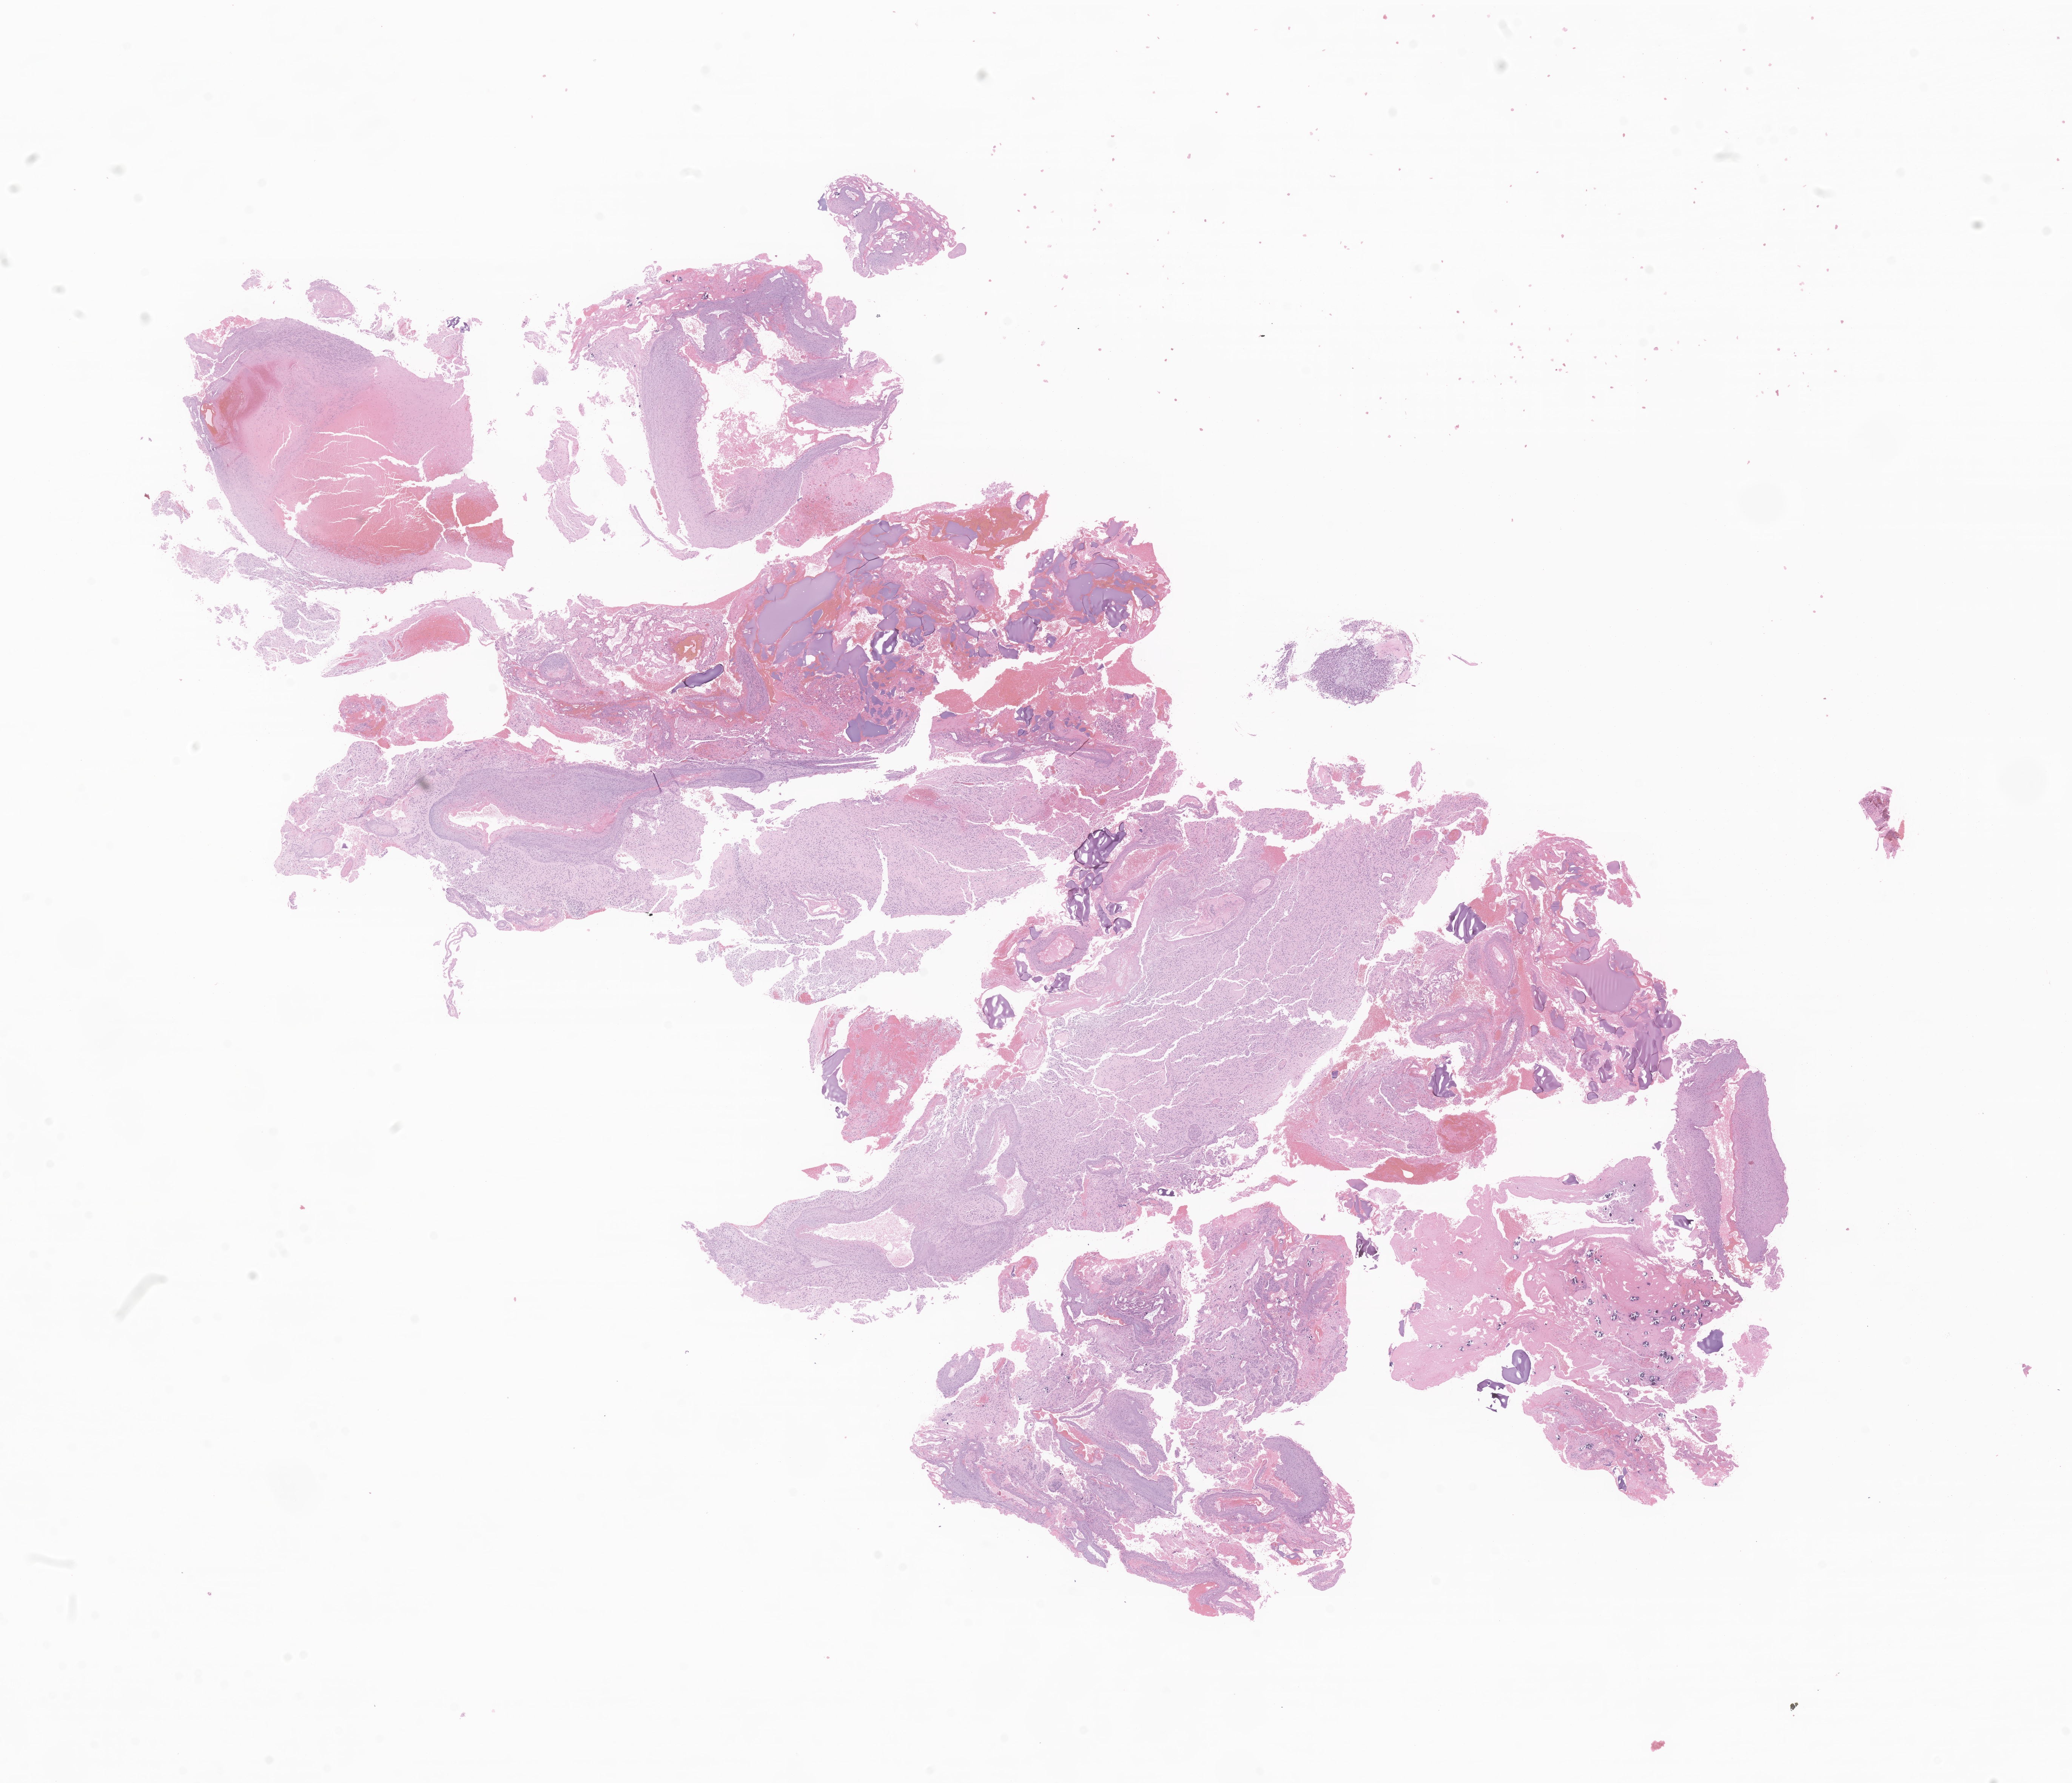
H&E whole-slide image of tumor tissue from the brain, a low-resolution overview of the entire scanned area, about 23.1 x 19.9 mm, FFPE section. Patient female; age 143 months (11 years 11 months).
Diagnosis (ICD-O-3 morphology term): Pilocytic astrocytoma.